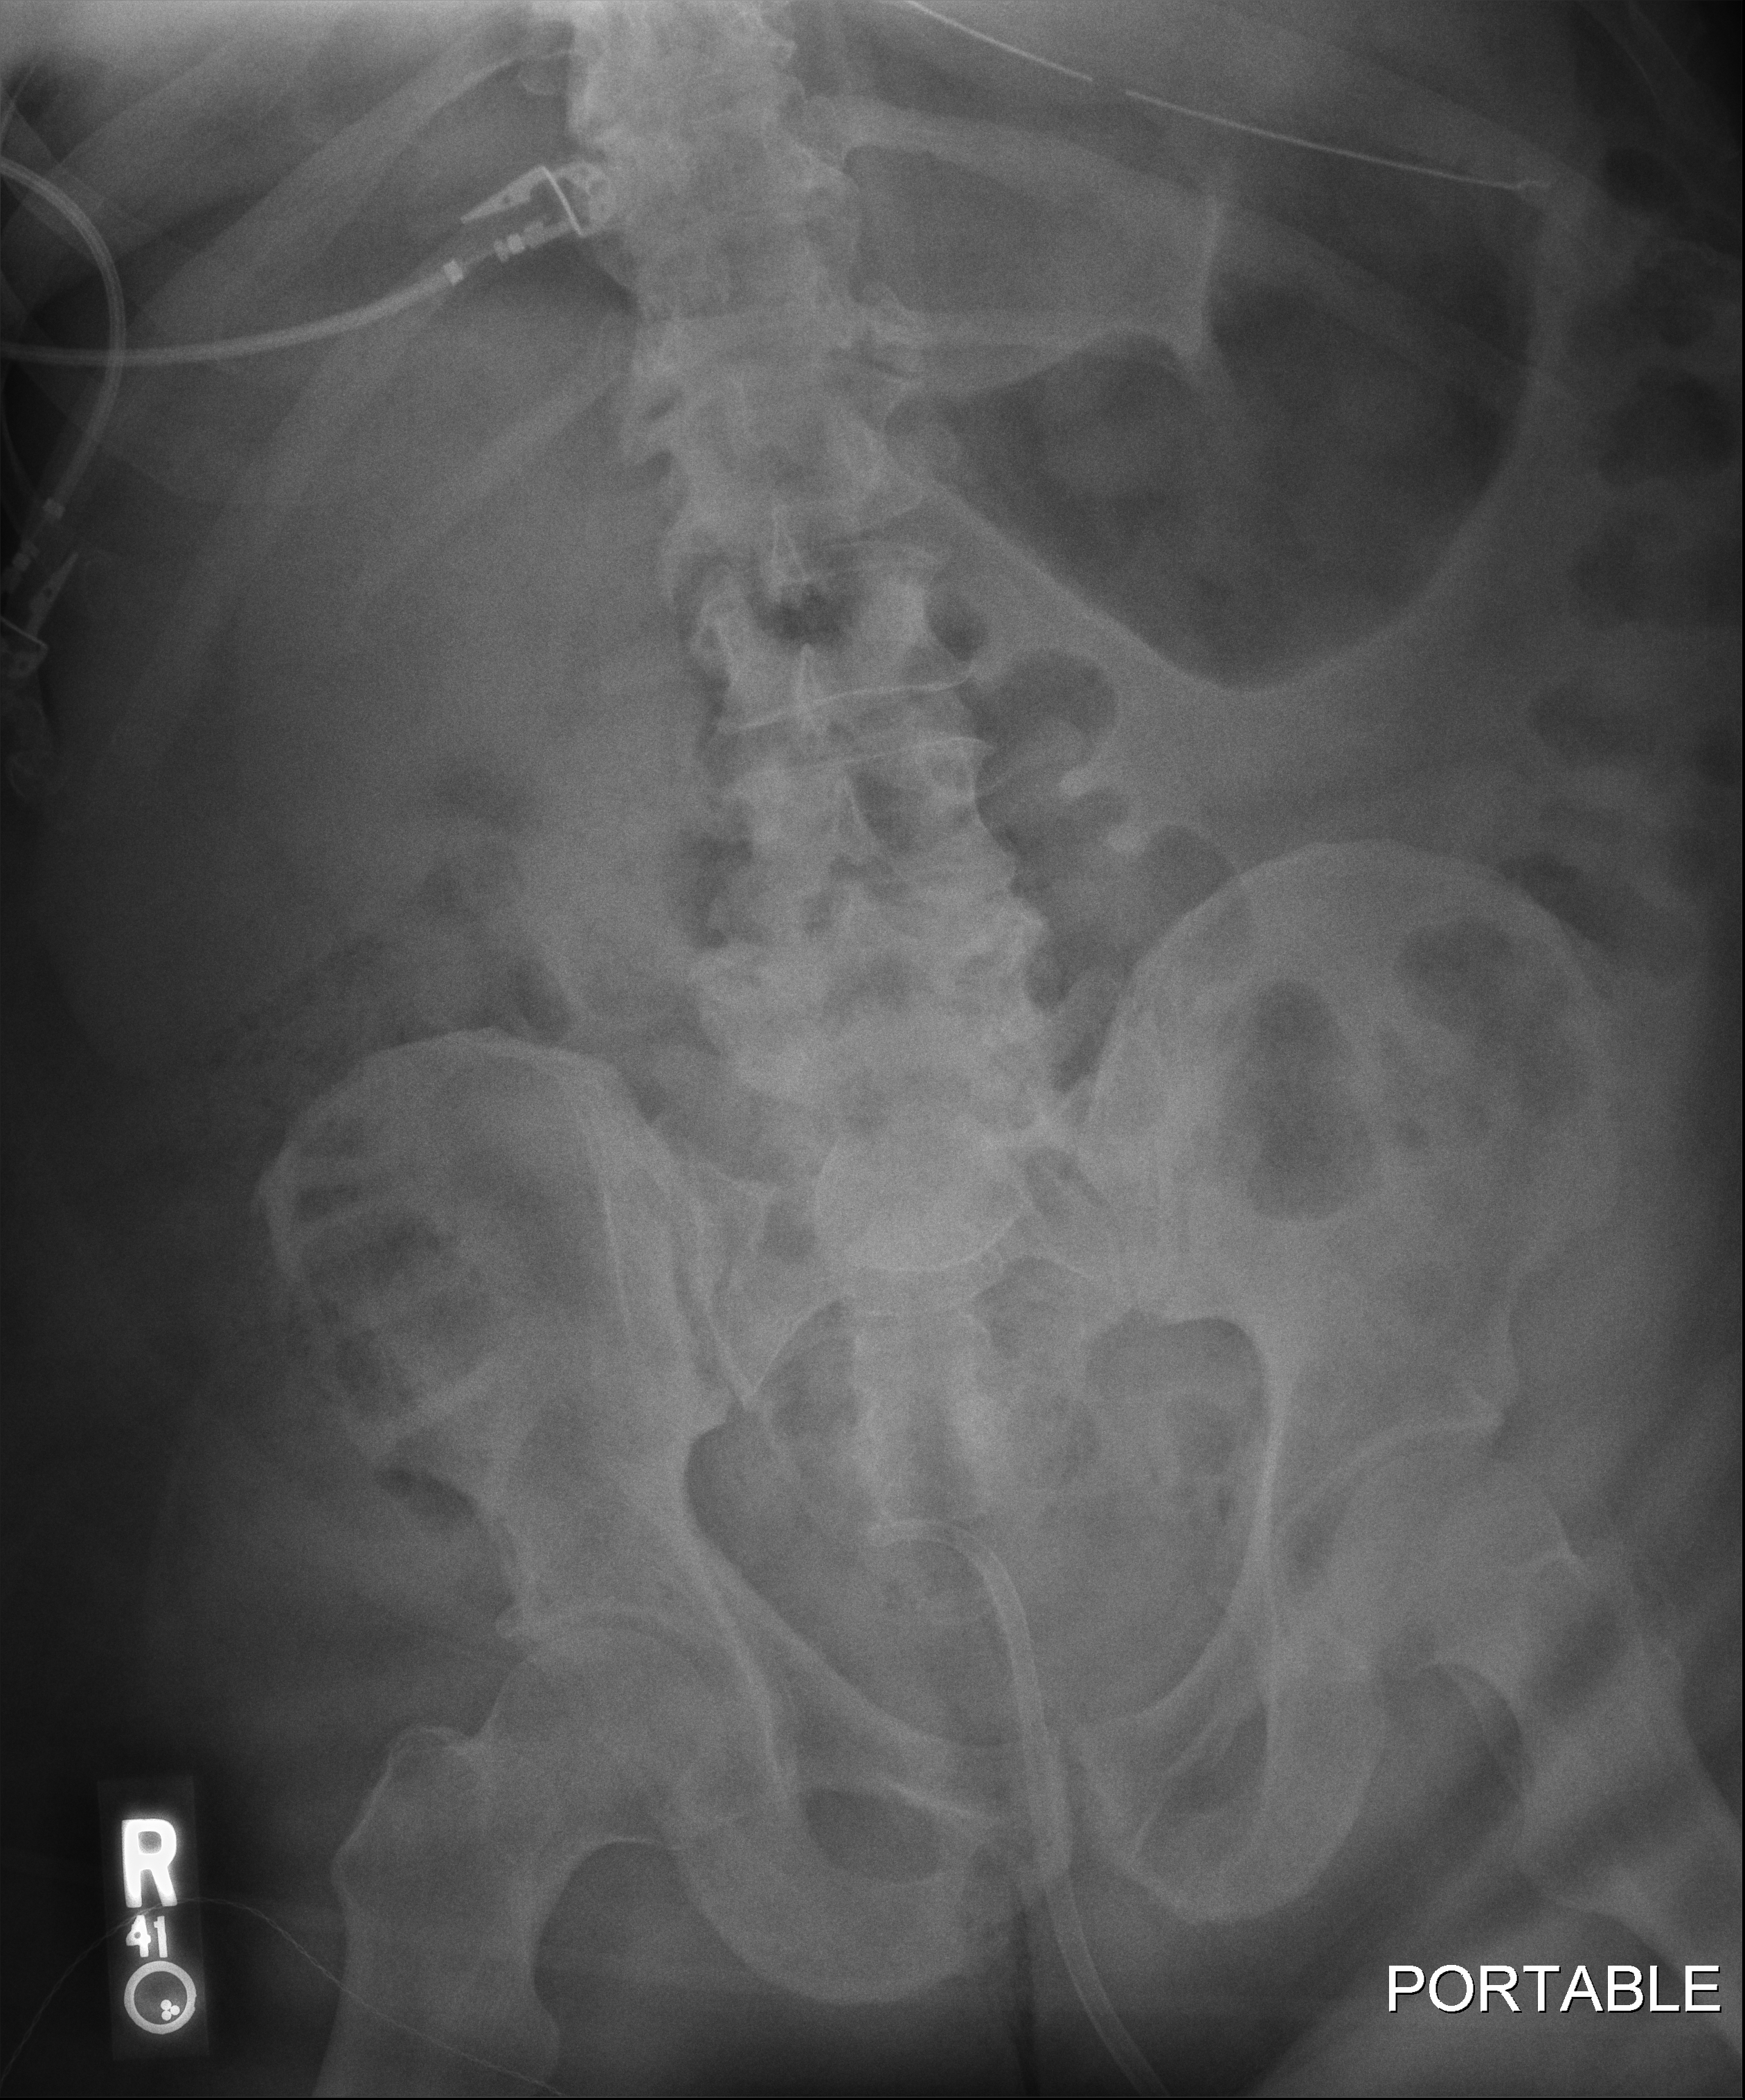
Abdomen radiograph, anteroposterior (AP) projection. Patient hospitalised with COVID-19, aged 18–59 years.
Hospital-stay facts (about this admission, not read from this image; timing relative to this image not recorded): admitted to intensive care during this hospital stay: yes; mechanically ventilated during this hospital stay: yes.